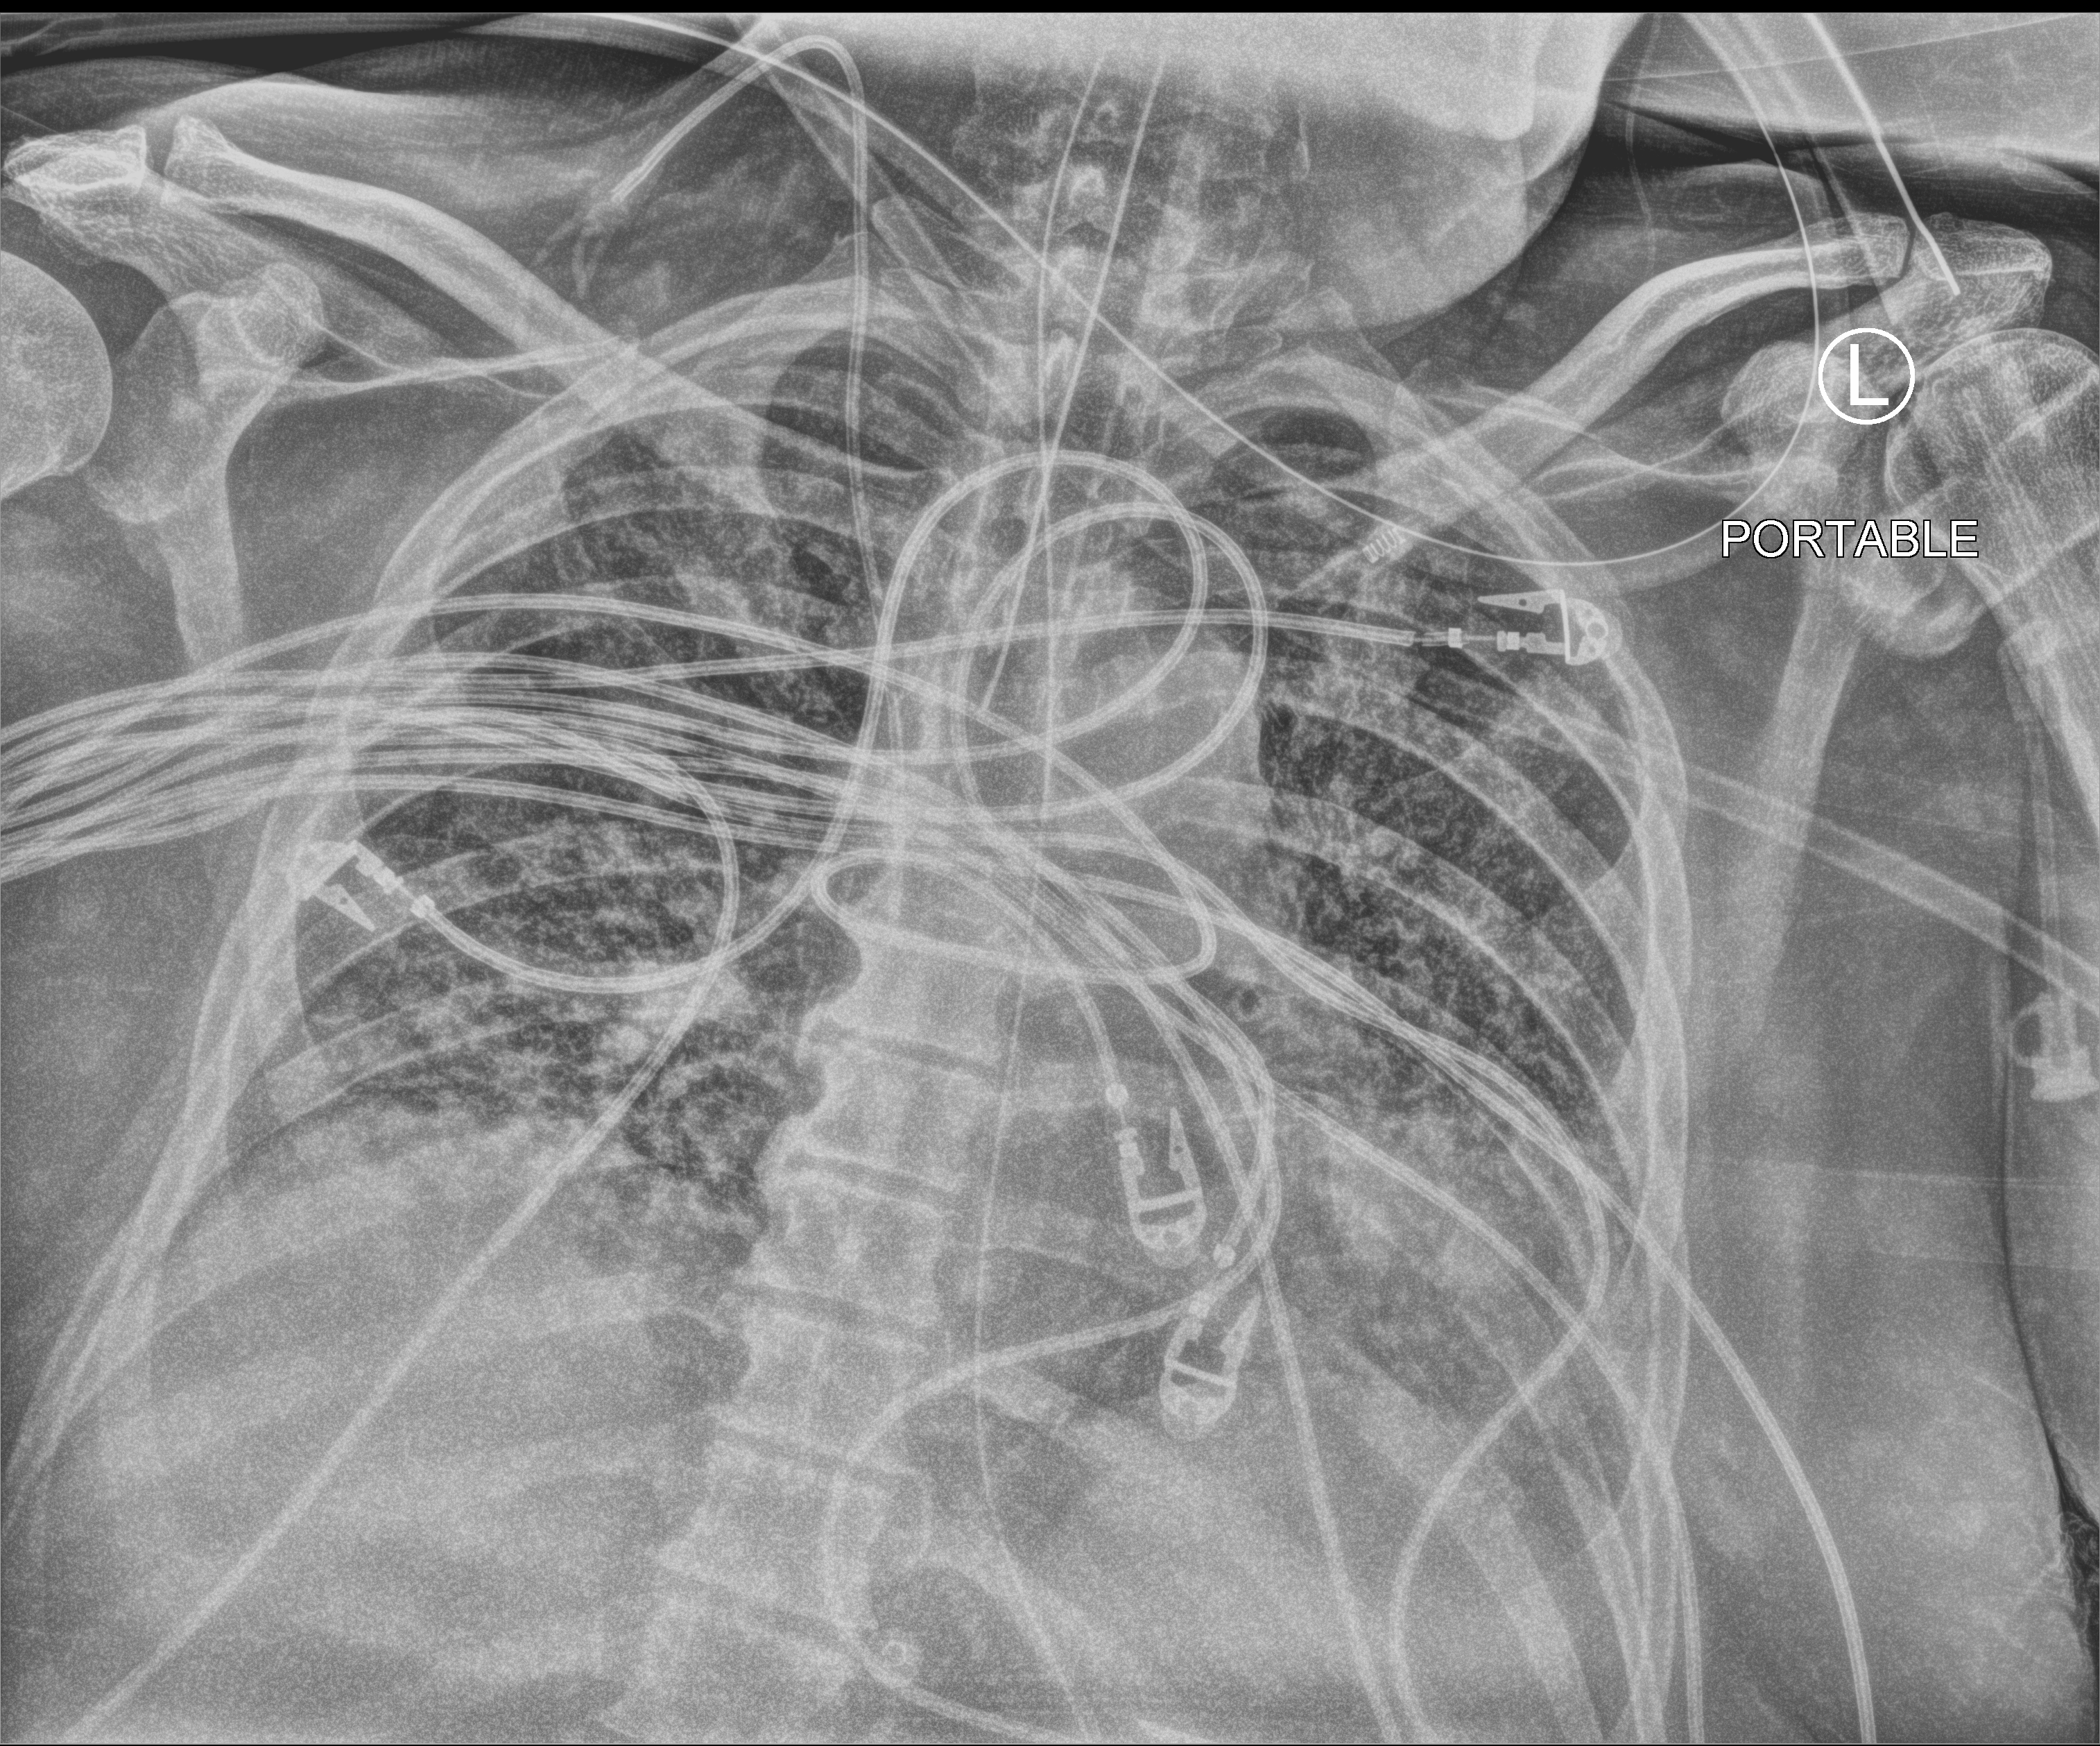
Bedside chest radiograph (computed radiography), anteroposterior (AP) projection. Patient hospitalised with COVID-19; male, aged 60–74 years.
Hospital-stay facts (about this admission, not read from this image; timing relative to this image not recorded):
- diabetes (admission record): no
- hypertension (admission record): yes